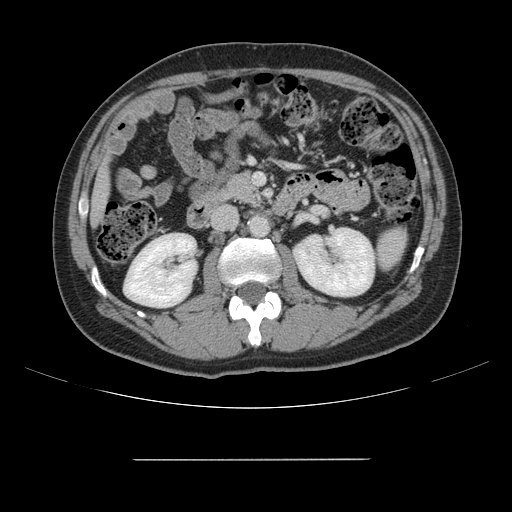
Contrast-enhanced abdominal CT, one axial slice; 120 kVp; intravenous contrast given; soft-tissue window (W 400 / L 40 HU); 512 × 512 image matrix. Male patient, age 54 years. From the clinical record (not read from this slice): diagnosis: colorectal cancer liver metastases, imaged before liver resection; multiple liver metastases: yes; largest metastasis: 1 cm.
Annotated regions visible in this slice (outlined manually by an expert reader):
- liver: bounding box <93,171,107,218> (left, top, right, bottom; pixels)
- planned liver remnant (the part of the liver to remain after resection): <93,173,107,220>